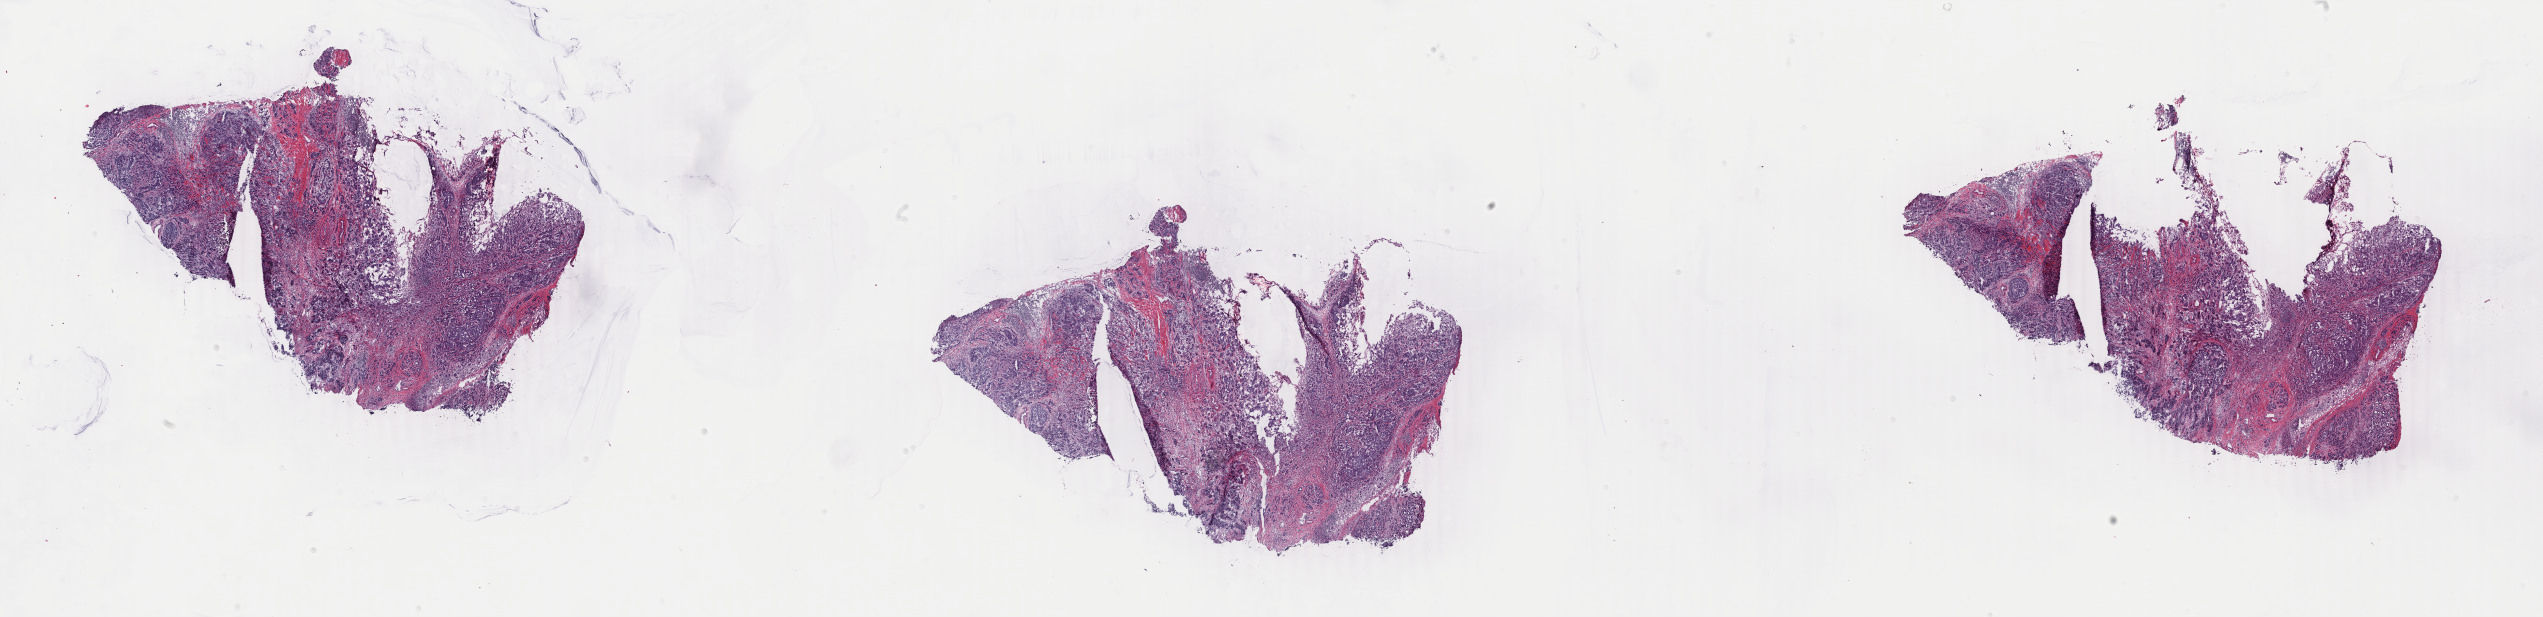
Digitized Hematoxylin and eosin (H&E) stained tissue section (whole slide), a low-resolution overview of the entire scanned area, about 40.5 x 9.8 mm (slide scanned at 40x). Frozen section from the top of the tissue portion. Primary tumour sample from the breast. Female, age 32 years at initial diagnosis. Pathologist review of this section (percent, as recorded): tumour cells 85%, tumour nuclei 85%, normal cells 0%, stromal cells 14%, necrosis 1%. Infiltration values recorded for this section: lymphocyte infiltration 1%, monocyte infiltration 0%, neutrophil infiltration 0%.
Histologic diagnosis: Infiltrating duct carcinoma, NOS. AJCC pathologic stage: IA. Laterality: left. Lymph nodes positive (case pathology): 0 of 14 examined.